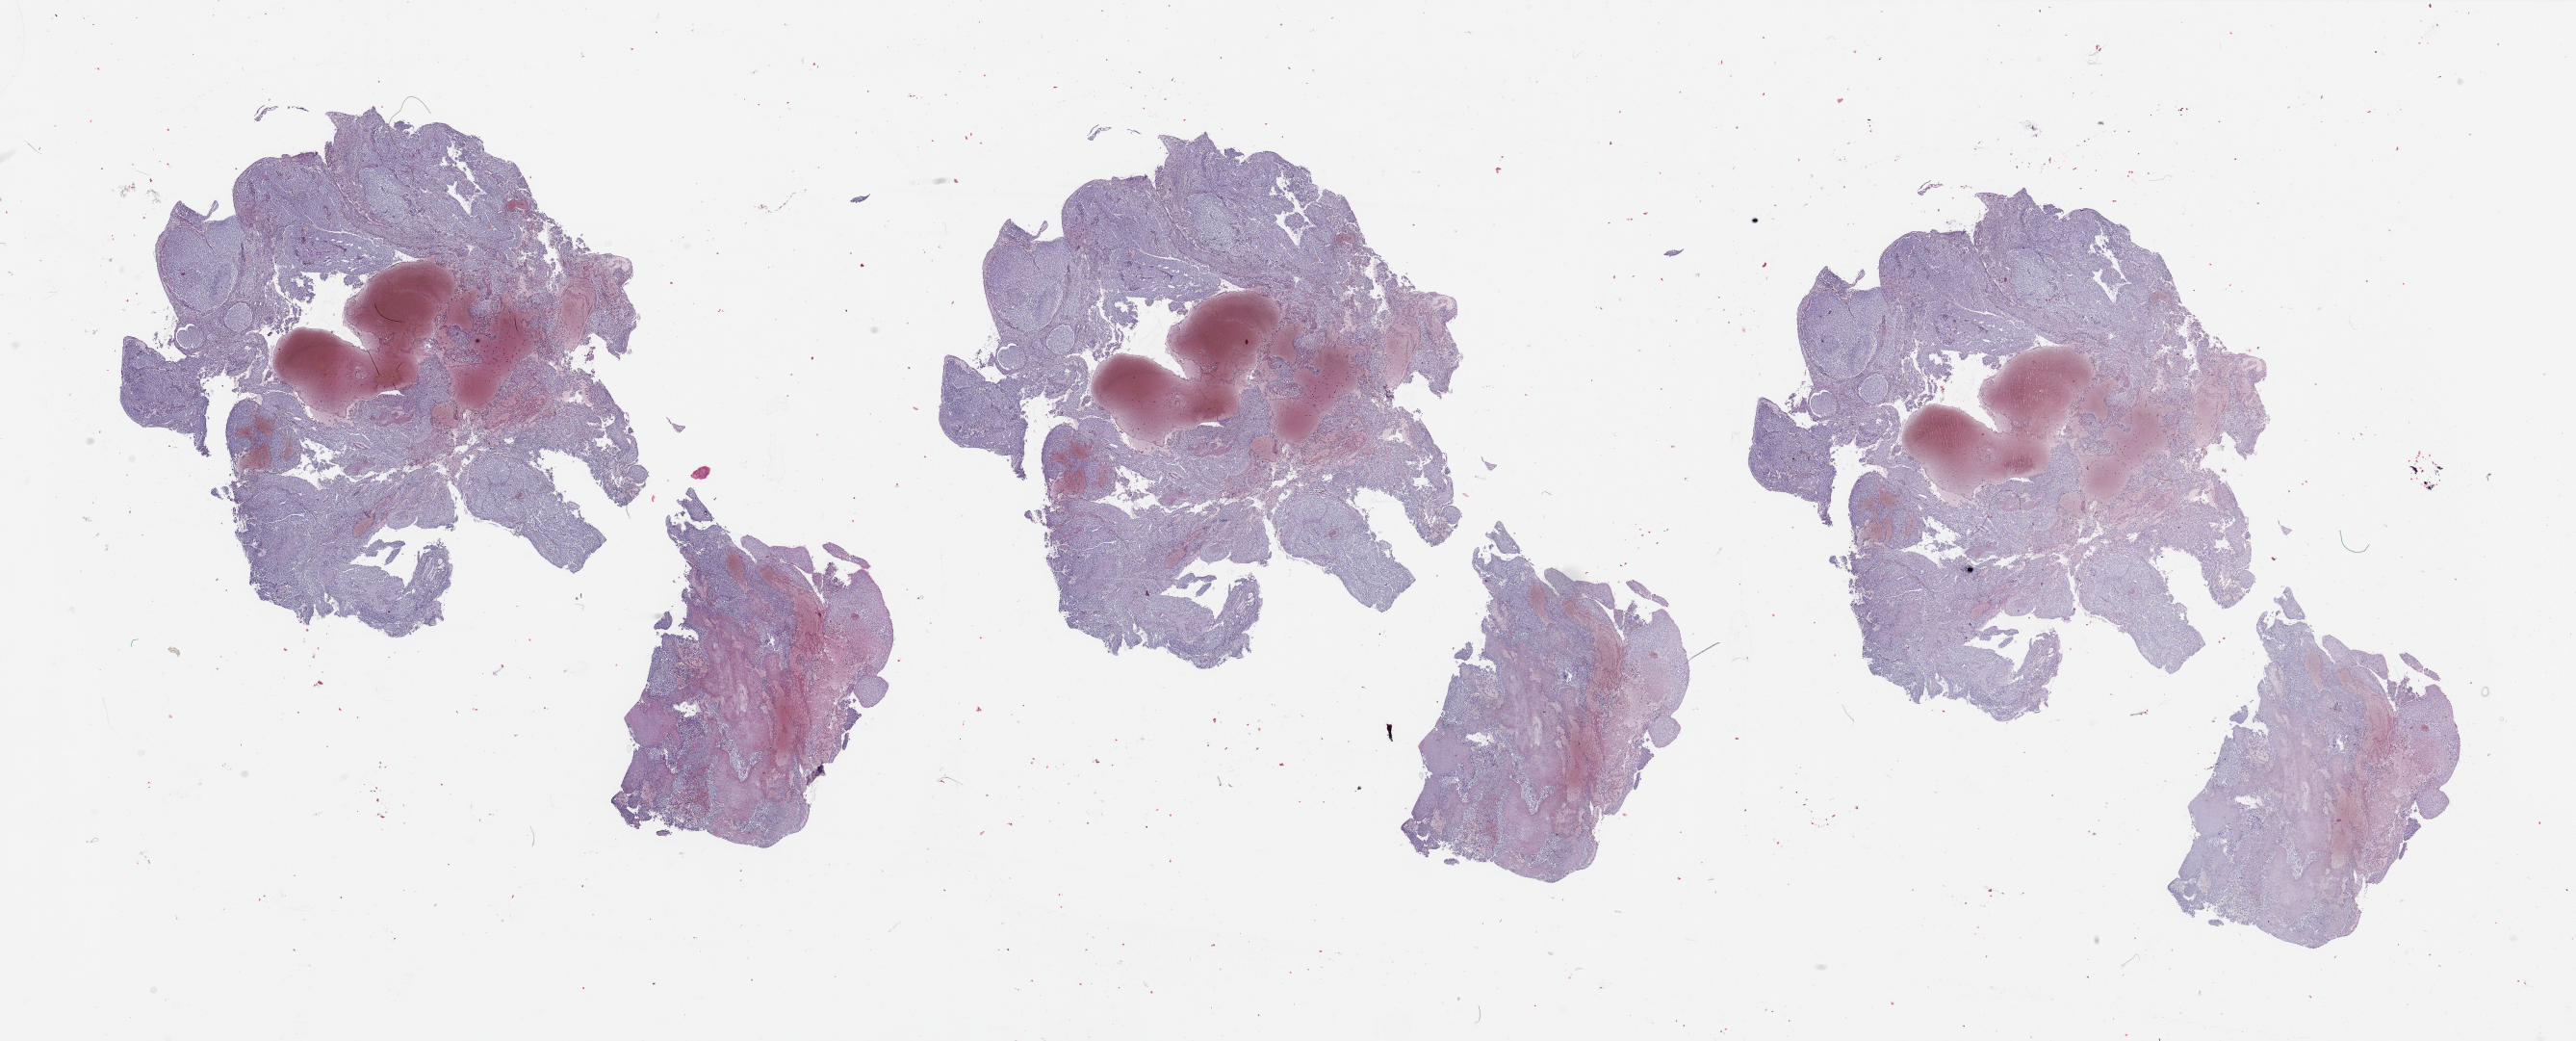
Hematoxylin and eosin (H&E) stained whole-slide image — shown as a low-resolution overview of the whole scanned area (about 42.3 x 17.1 mm). Brain, tumour tissue. 40-year-old male patient.
Primary tumour site (as recorded): parietal lobe. Histologic diagnosis: Glioblastoma.